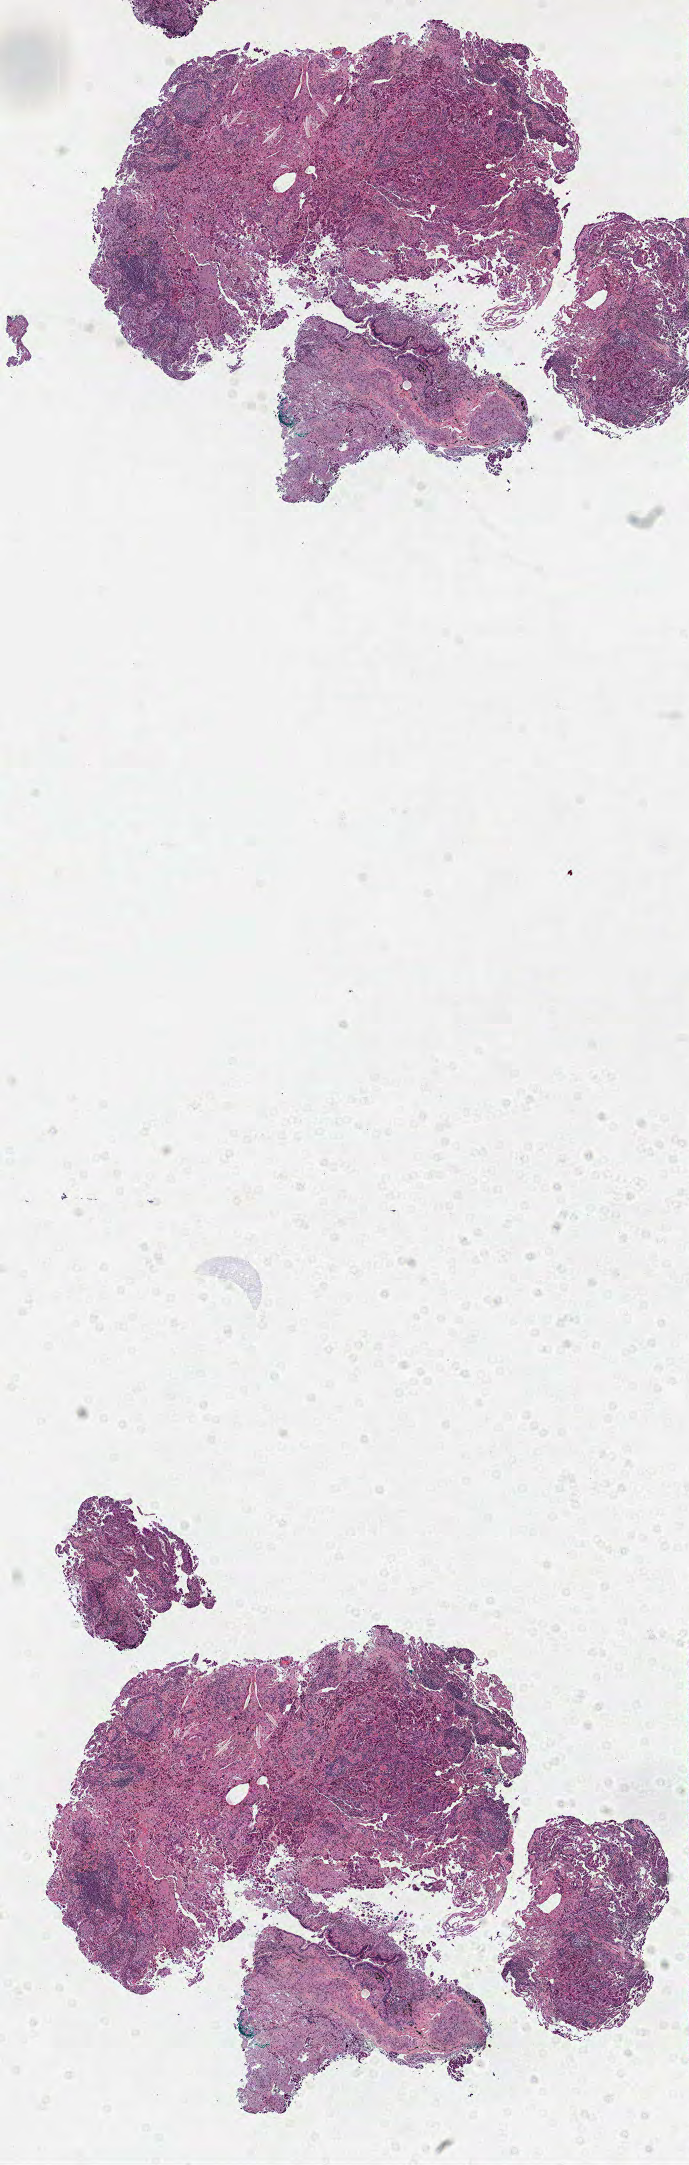
Digitized H&E-stained tissue section (whole slide) — whole scanned area (about 5.6 x 17.5 mm, acquisition: 40x scan) shown as a low-resolution overview. Formalin-fixed paraffin-embedded (FFPE) diagnostic section. Lung, primary tumour sample. Female patient; age at initial diagnosis 71 years.
AJCC pathologic stage: IA (7th edition). Laterality: right. Diagnosis: Adenocarcinoma, NOS (upper lobe, lung). TNM: T1 N0 M0.